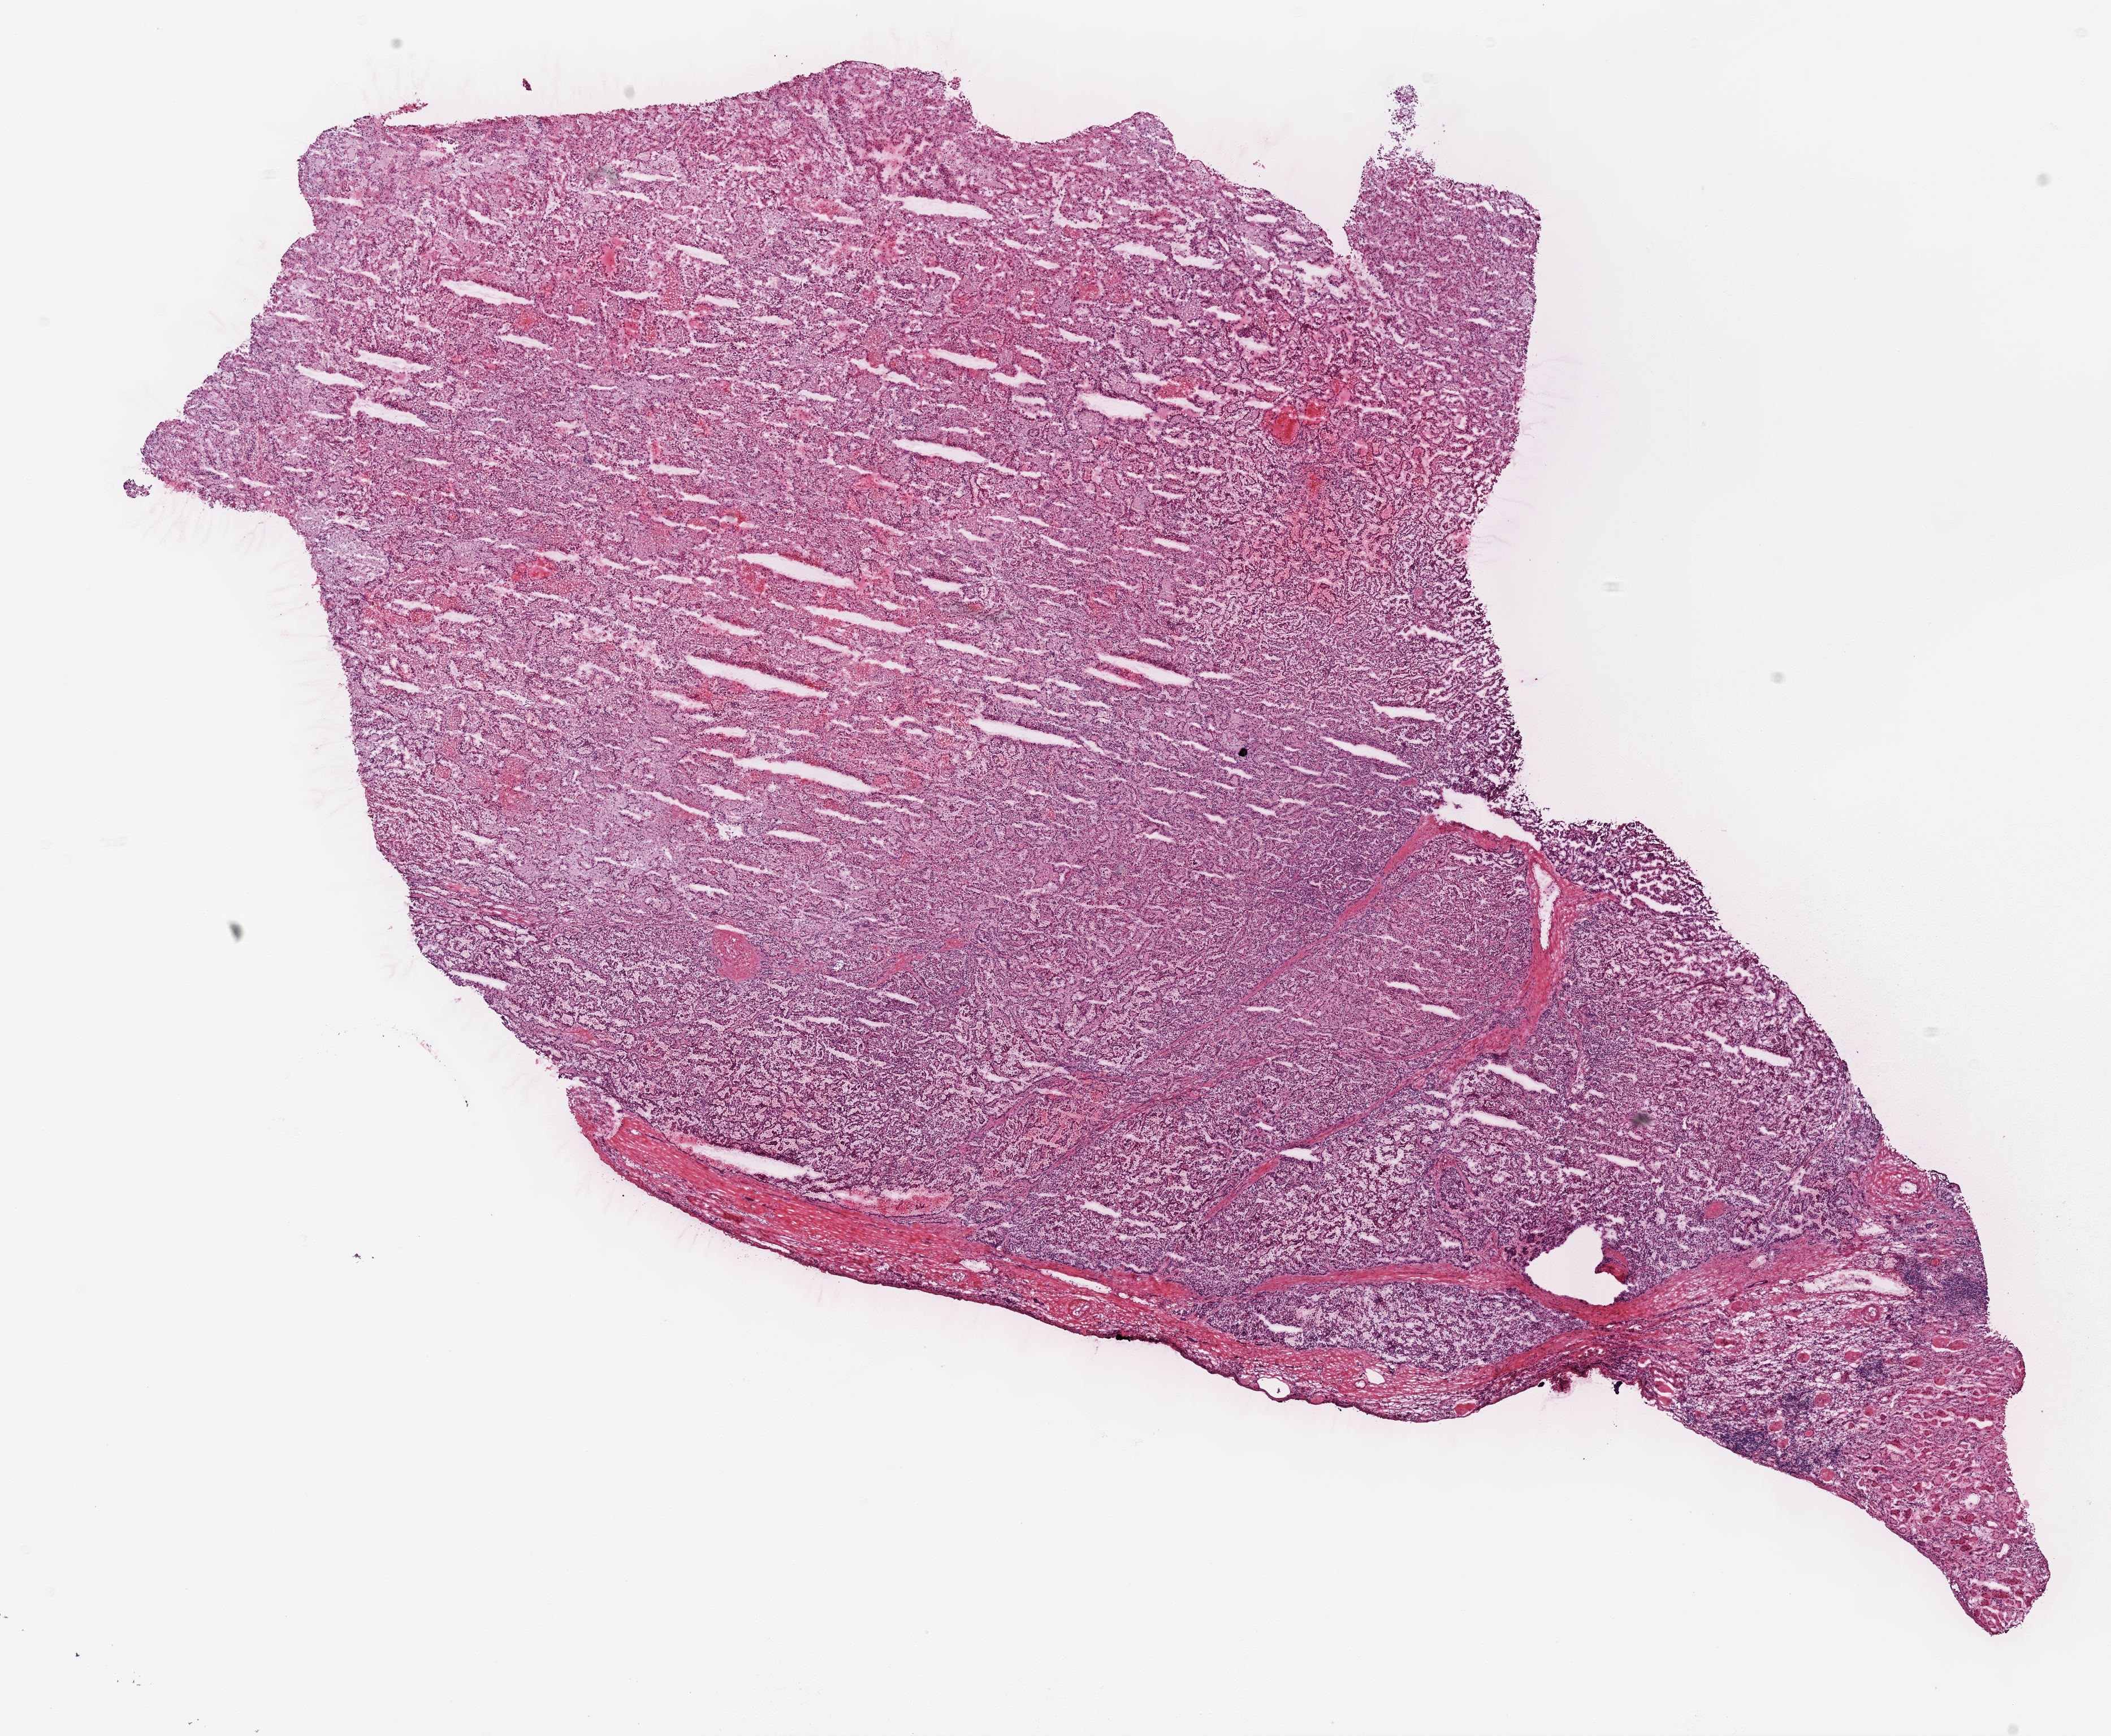
Digitized H&E tissue section (whole slide), low-resolution overview of the scanned area, about 15.1 x 12.4 mm (slide scanned at 40x), formalin-fixed paraffin-embedded (FFPE) diagnostic section, sample: primary tumour, kidney. Male patient; age at initial diagnosis 67 years.
Histologic diagnosis: Papillary adenocarcinoma, NOS.